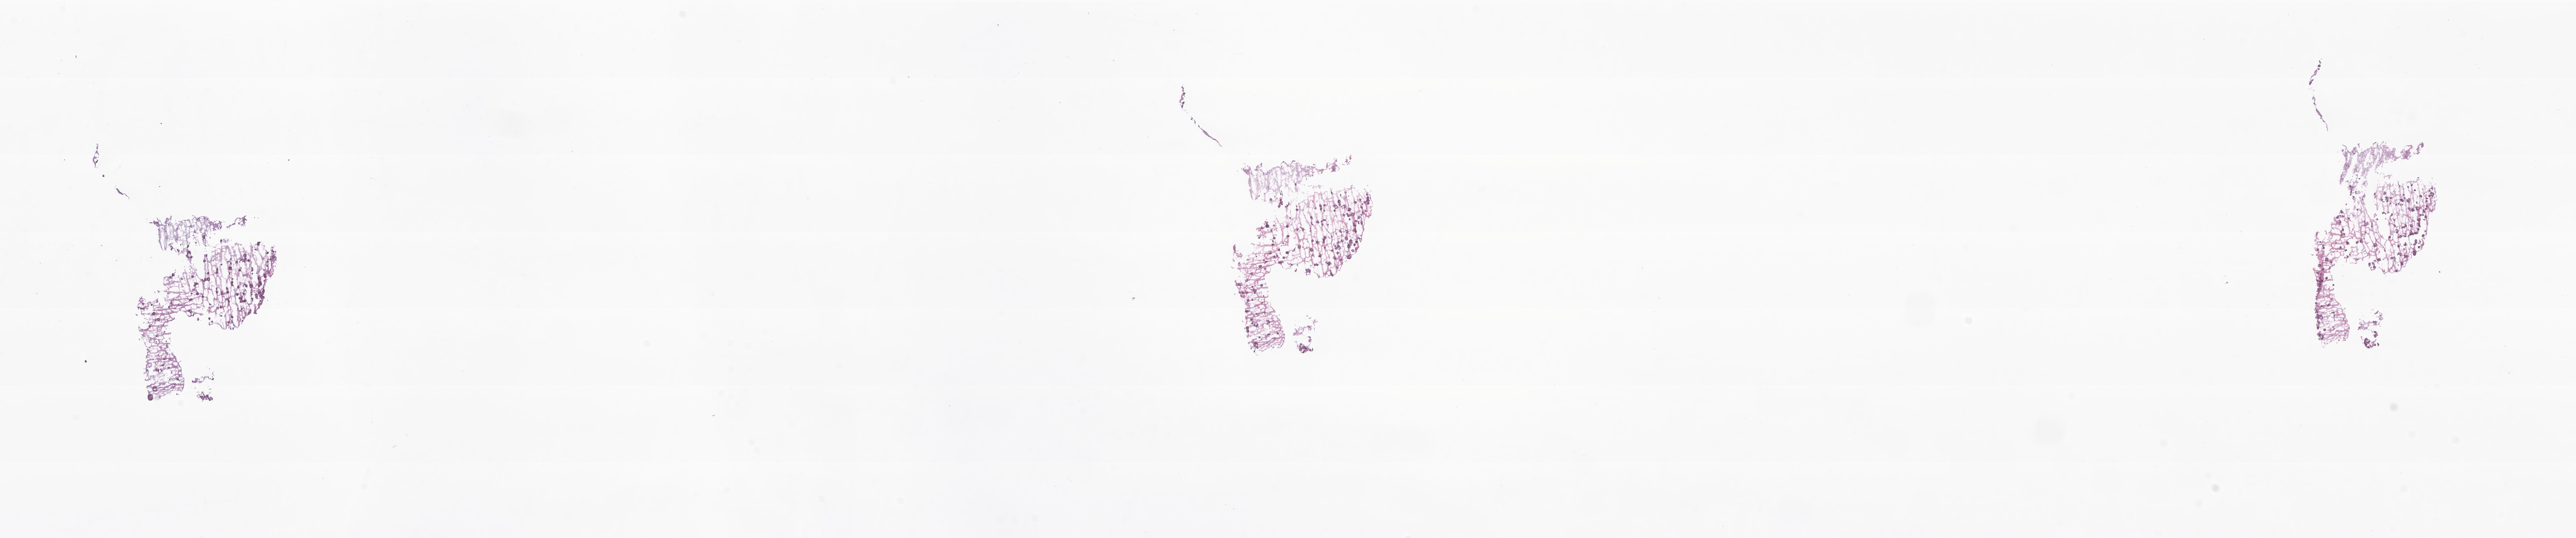
Hematoxylin and eosin (H&E) whole-slide image of tumor tissue from the brain, whole scanned area (about 35.7 x 7.5 mm) shown as a low-resolution overview. Frozen section (OCT-embedded). Patient: male, age 139 months.
Diagnosis (ICD-O-3 morphology term): Ganglioglioma, NOS.